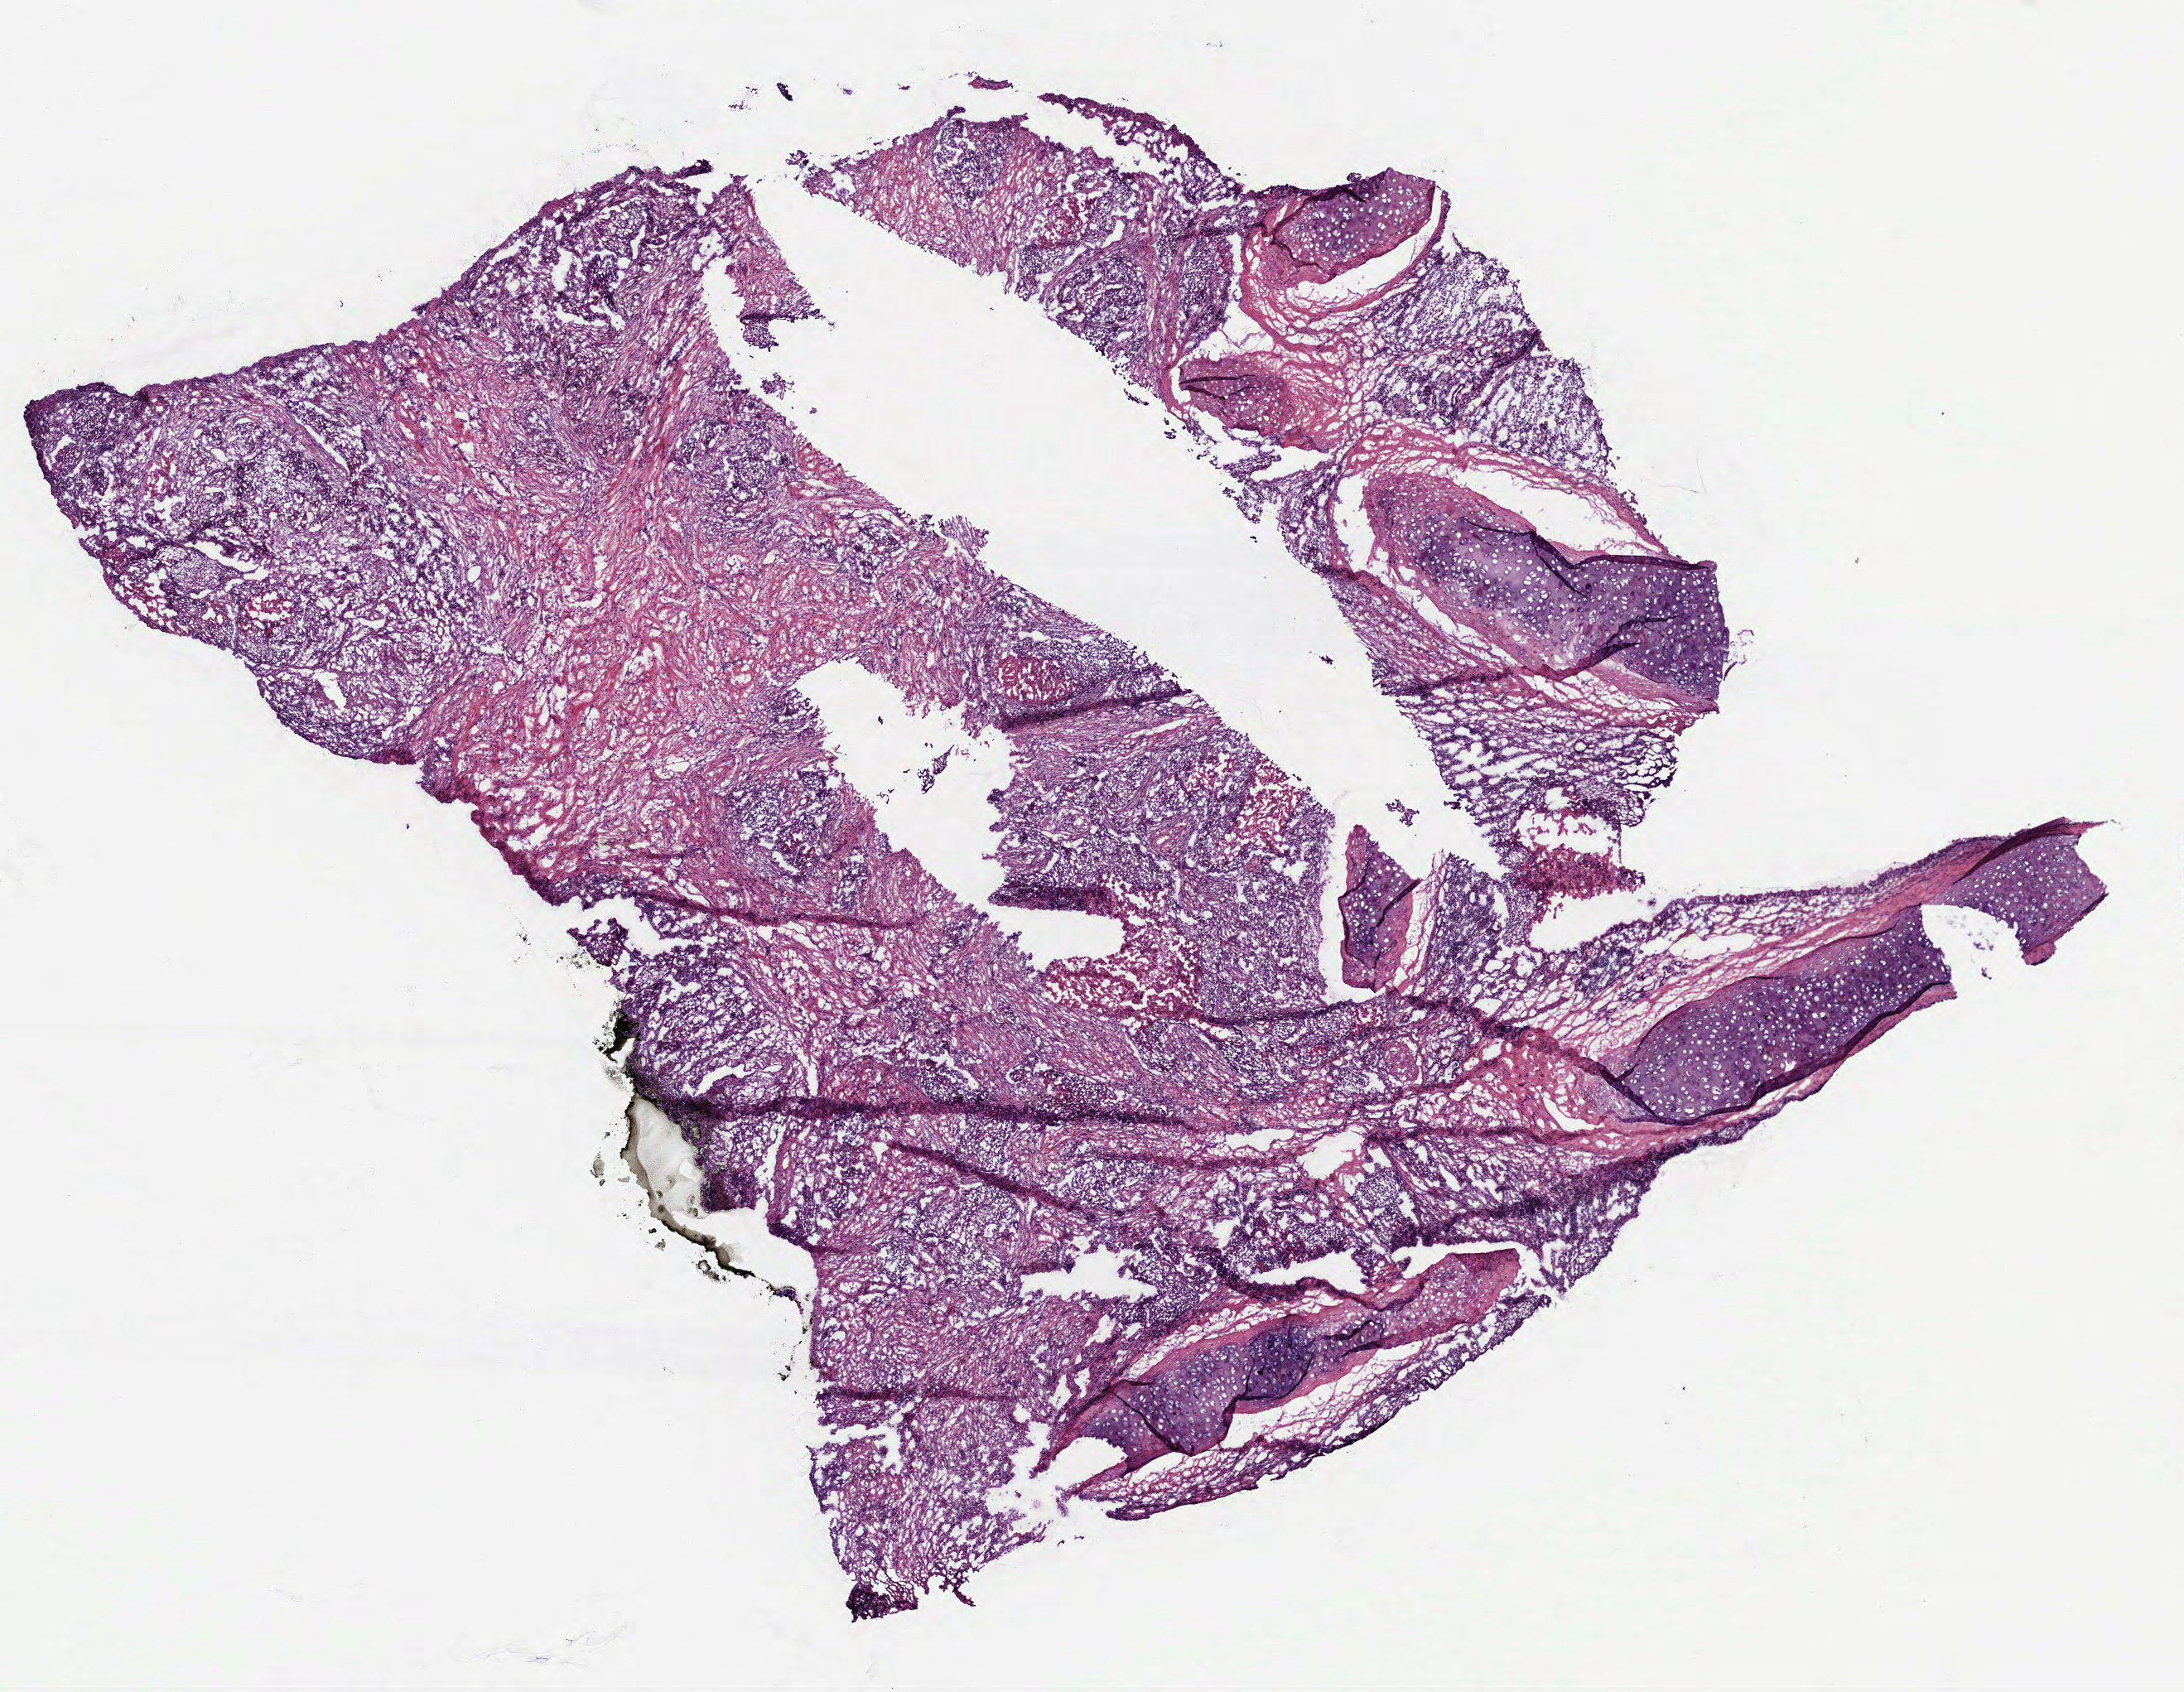
Digitized Hematoxylin and eosin (H&E) stained tissue section (whole slide) — low-resolution overview of the scanned area, about 10.6 x 8.2 mm, frozen section from the bottom of the tissue portion, primary tumour sample from the lung. Female, age 62 years at initial diagnosis. Pathologist review of this section (percent, as recorded): tumour cells 50%, tumour nuclei 40%, normal cells 24%, stromal cells 21%, necrosis 5%. Inflammatory infiltration, as recorded: lymphocyte infiltration 20%, monocyte infiltration 10%, neutrophil infiltration 2%.
TNM: T4 N2 M0. AJCC pathologic stage: IIIB (6th edition). Pathologic diagnosis: Squamous cell carcinoma, keratinizing, NOS.